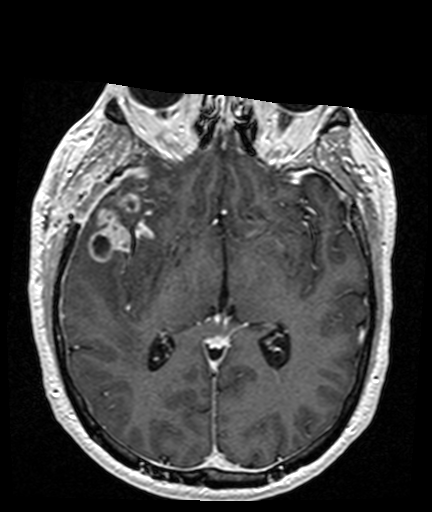
Brain MRI from a brain-tumour surgery series, one axial slice; slice 91 of 176 in the series (ordered by position); T1-weighted post-contrast; 1 mm slice thickness; 432 × 512 image matrix. Case-level facts recorded for this patient, not image findings: histopathology: Glioblastoma; WHO grade: 4; IDH mutation: no.
Structures marked on this image (manually delineated by an expert):
- tumour: bounding box (x1, y1, x2, y2) in pixels: (88, 190, 153, 263)